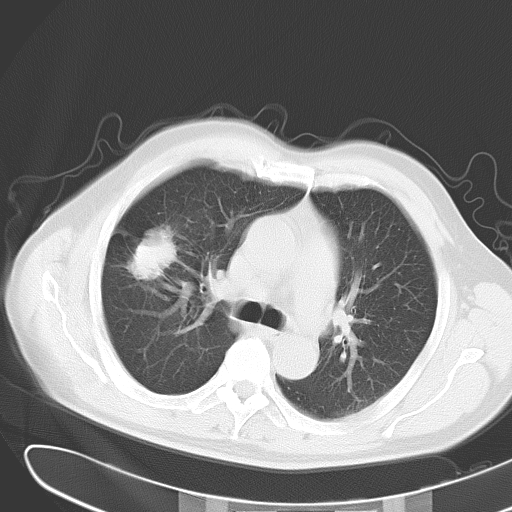
Chest CT, one axial slice; position 20 of 31 along the scan axis; reconstruction kernel B70f; 120 kVp; lung window (W 1500 / L -600 HU); 10 mm slice thickness; 512 × 512 image matrix. Male patient, age 59 years. Case-level facts recorded for this patient, not image findings: clinical TNM (as recorded): T2 N3 M0.
Annotated regions visible in this slice (bounding box drawn by a radiologist):
- lung tumour (recorded histology: adenocarcinoma): bounding box <132,223,175,285> (left, top, right, bottom; pixels)